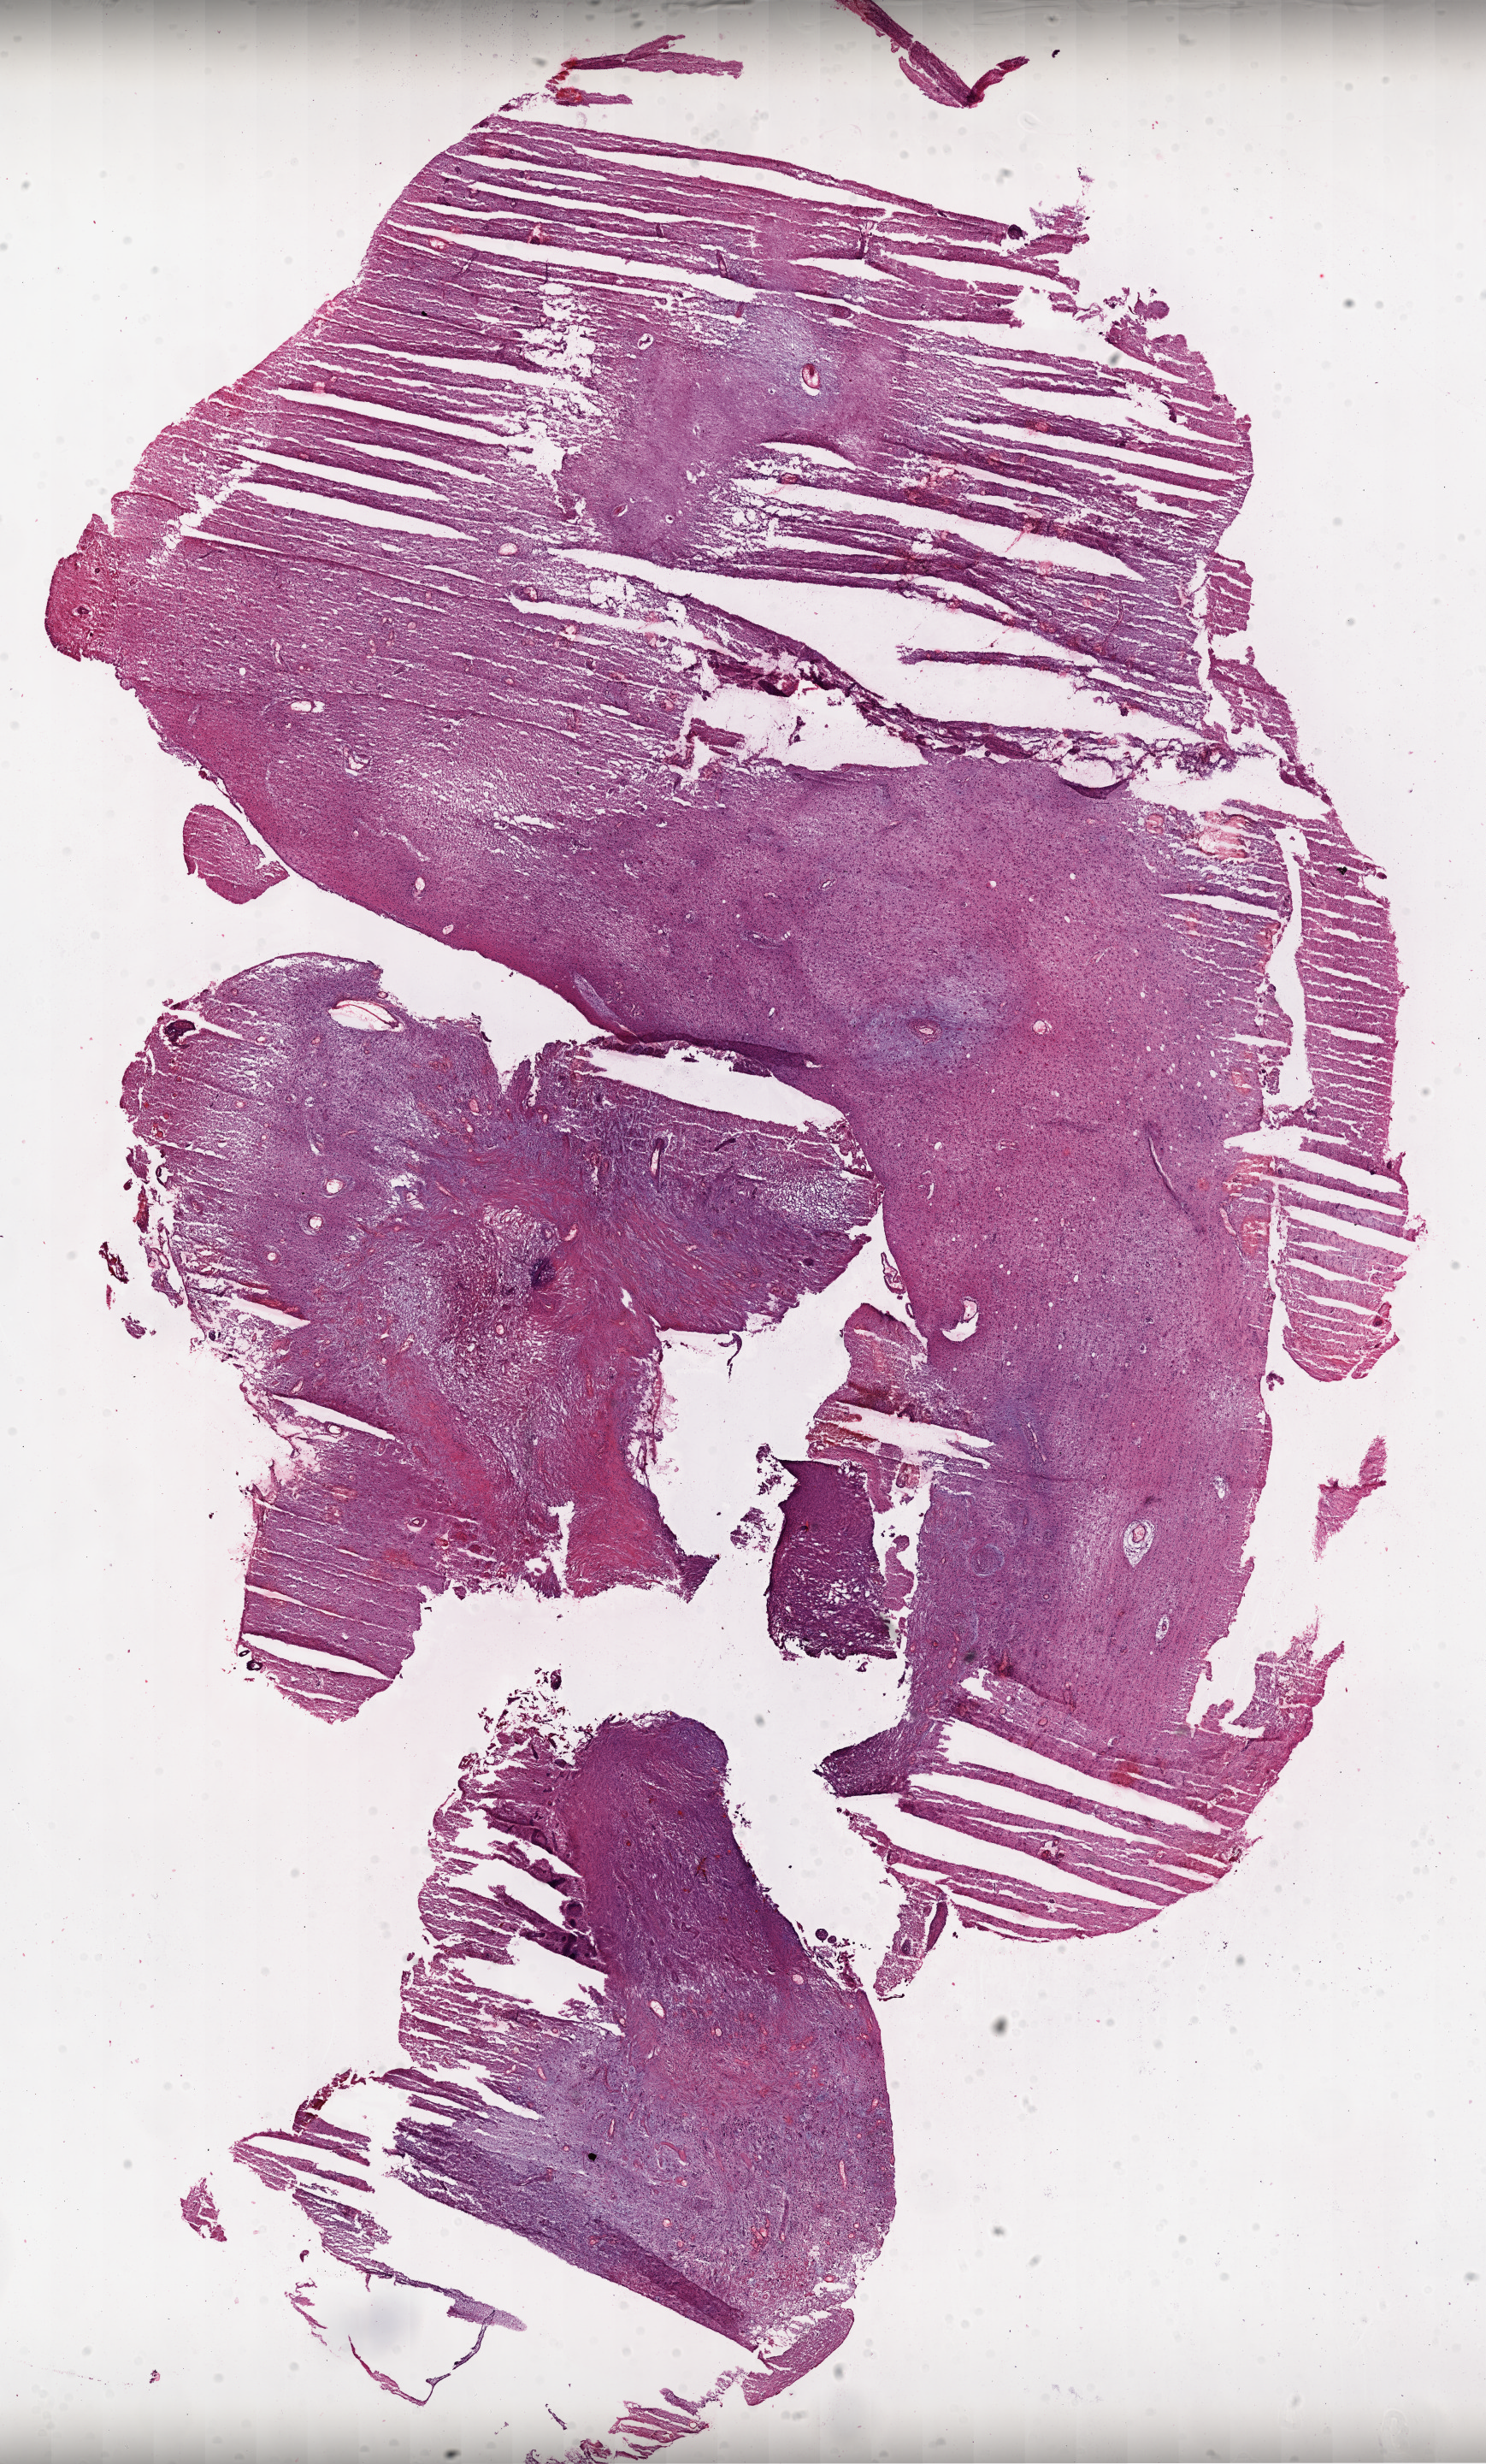
Digitized H&E-stained tissue section (whole slide), a low-resolution overview of the entire scanned area, about 14.0 x 23.2 mm (slide scanned at 20x); frozen section from the top of the tissue portion; primary tumour sample from the brain. Male, age 56 years at initial diagnosis. Composition of this section per pathologist review: tumour cells 80%, tumour nuclei 90%, normal cells 0%, stromal cells 10%, necrosis 10%.
Pathologic diagnosis: Glioblastoma.